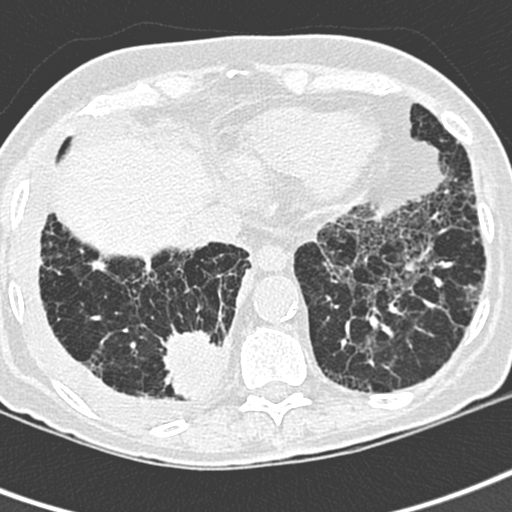
Low-dose screening chest CT, one axial slice; slice 74 of 220 in the series (ordered by position); 120 kVp; lung window (W 1500 / L -600 HU); 512 × 512 image matrix, field of view 288 × 288 mm.
Outlined on this slice (outlined manually by an expert reader):
- lesion 1 (tumor, lower lobe of right lung): bounding box (x1, y1, x2, y2) in pixels: (163, 330, 223, 399)